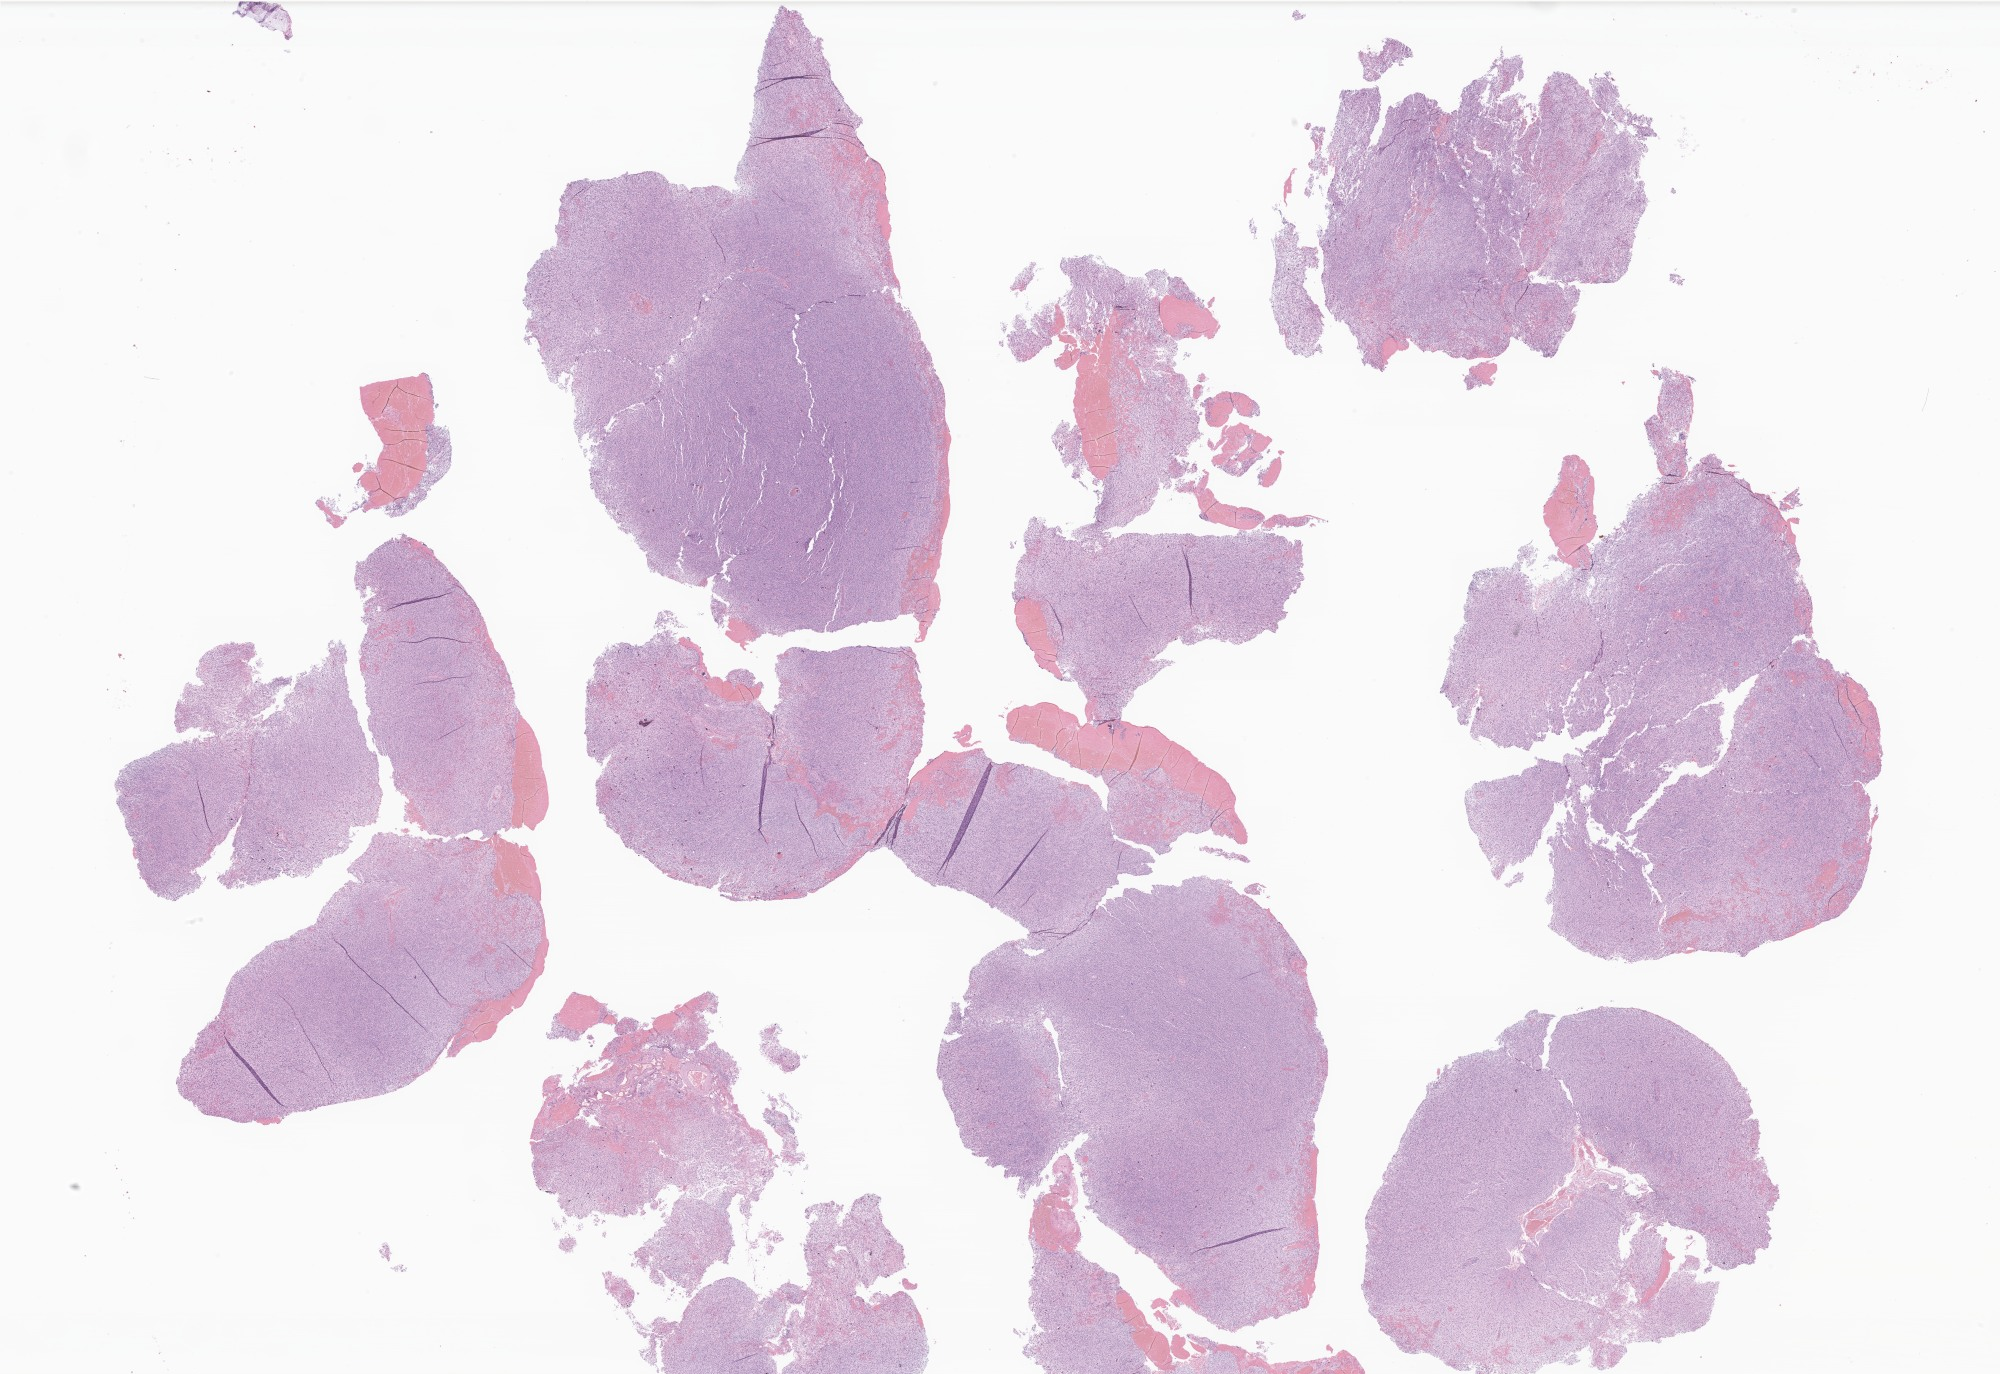
Digitized haematoxylin and eosin-stained section of tumor tissue from the frontal lobe — whole scanned area (about 33.7 x 23.2 mm) shown as a low-resolution overview, formalin-fixed paraffin-embedded section. Female patient, age 131 months (10 years 11 months).
Diagnosis (ICD-O-3 morphology term): Glioma, malignant.